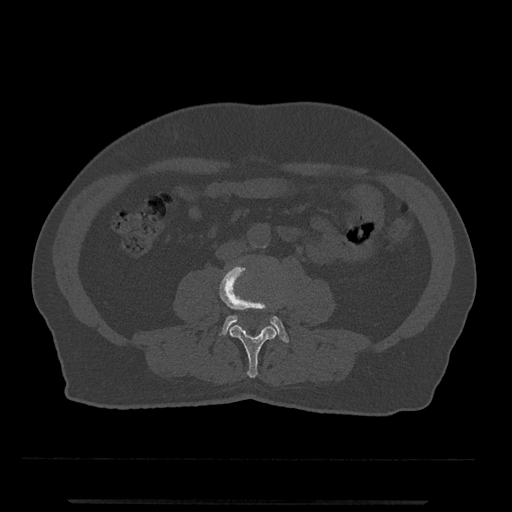
CT including the spine, one axial slice. Slice 178 of 797 in the series (ordered by position). Bone window (W 1800 / L 400 HU). 0.5 mm slice thickness. 512 × 512 image matrix, field of view 419 × 419 mm. Male patient, age 63 years. Case-level facts recorded for this patient, not image findings: primary cancer: prostate.
Outlined on this slice (semi-automatically segmented with operator editing):
- L3 vertebra: bounding box (x1, y1, x2, y2) in pixels: (219, 265, 283, 378)
- L4 vertebra: (220, 315, 289, 343)